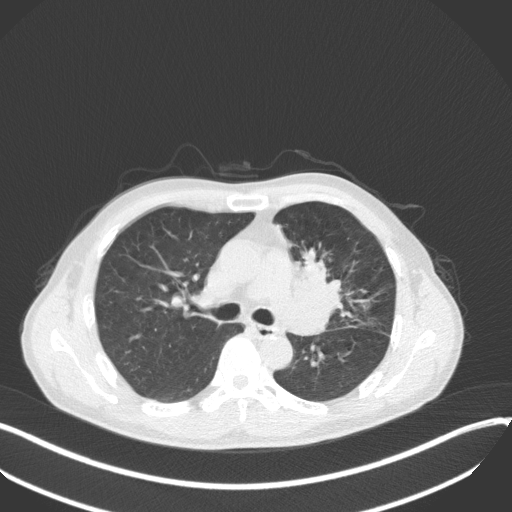
Chest CT, one axial slice. Slice 210 of 411 in the series (ordered by position). Reconstruction kernel B31f. 120 kVp. Lung window (W 1500 / L -600 HU). 512 × 512 image matrix, field of view 400 × 400 mm. Patient: male, 56 years. Case-level facts recorded for this patient, not image findings: clinical TNM (as recorded): T2a N0 M0.
Structures marked on this image (rectangle marked by the reading radiologist):
- lung tumour (recorded histology: squamous cell carcinoma): bounding box <289,246,350,341> (left, top, right, bottom; pixels)